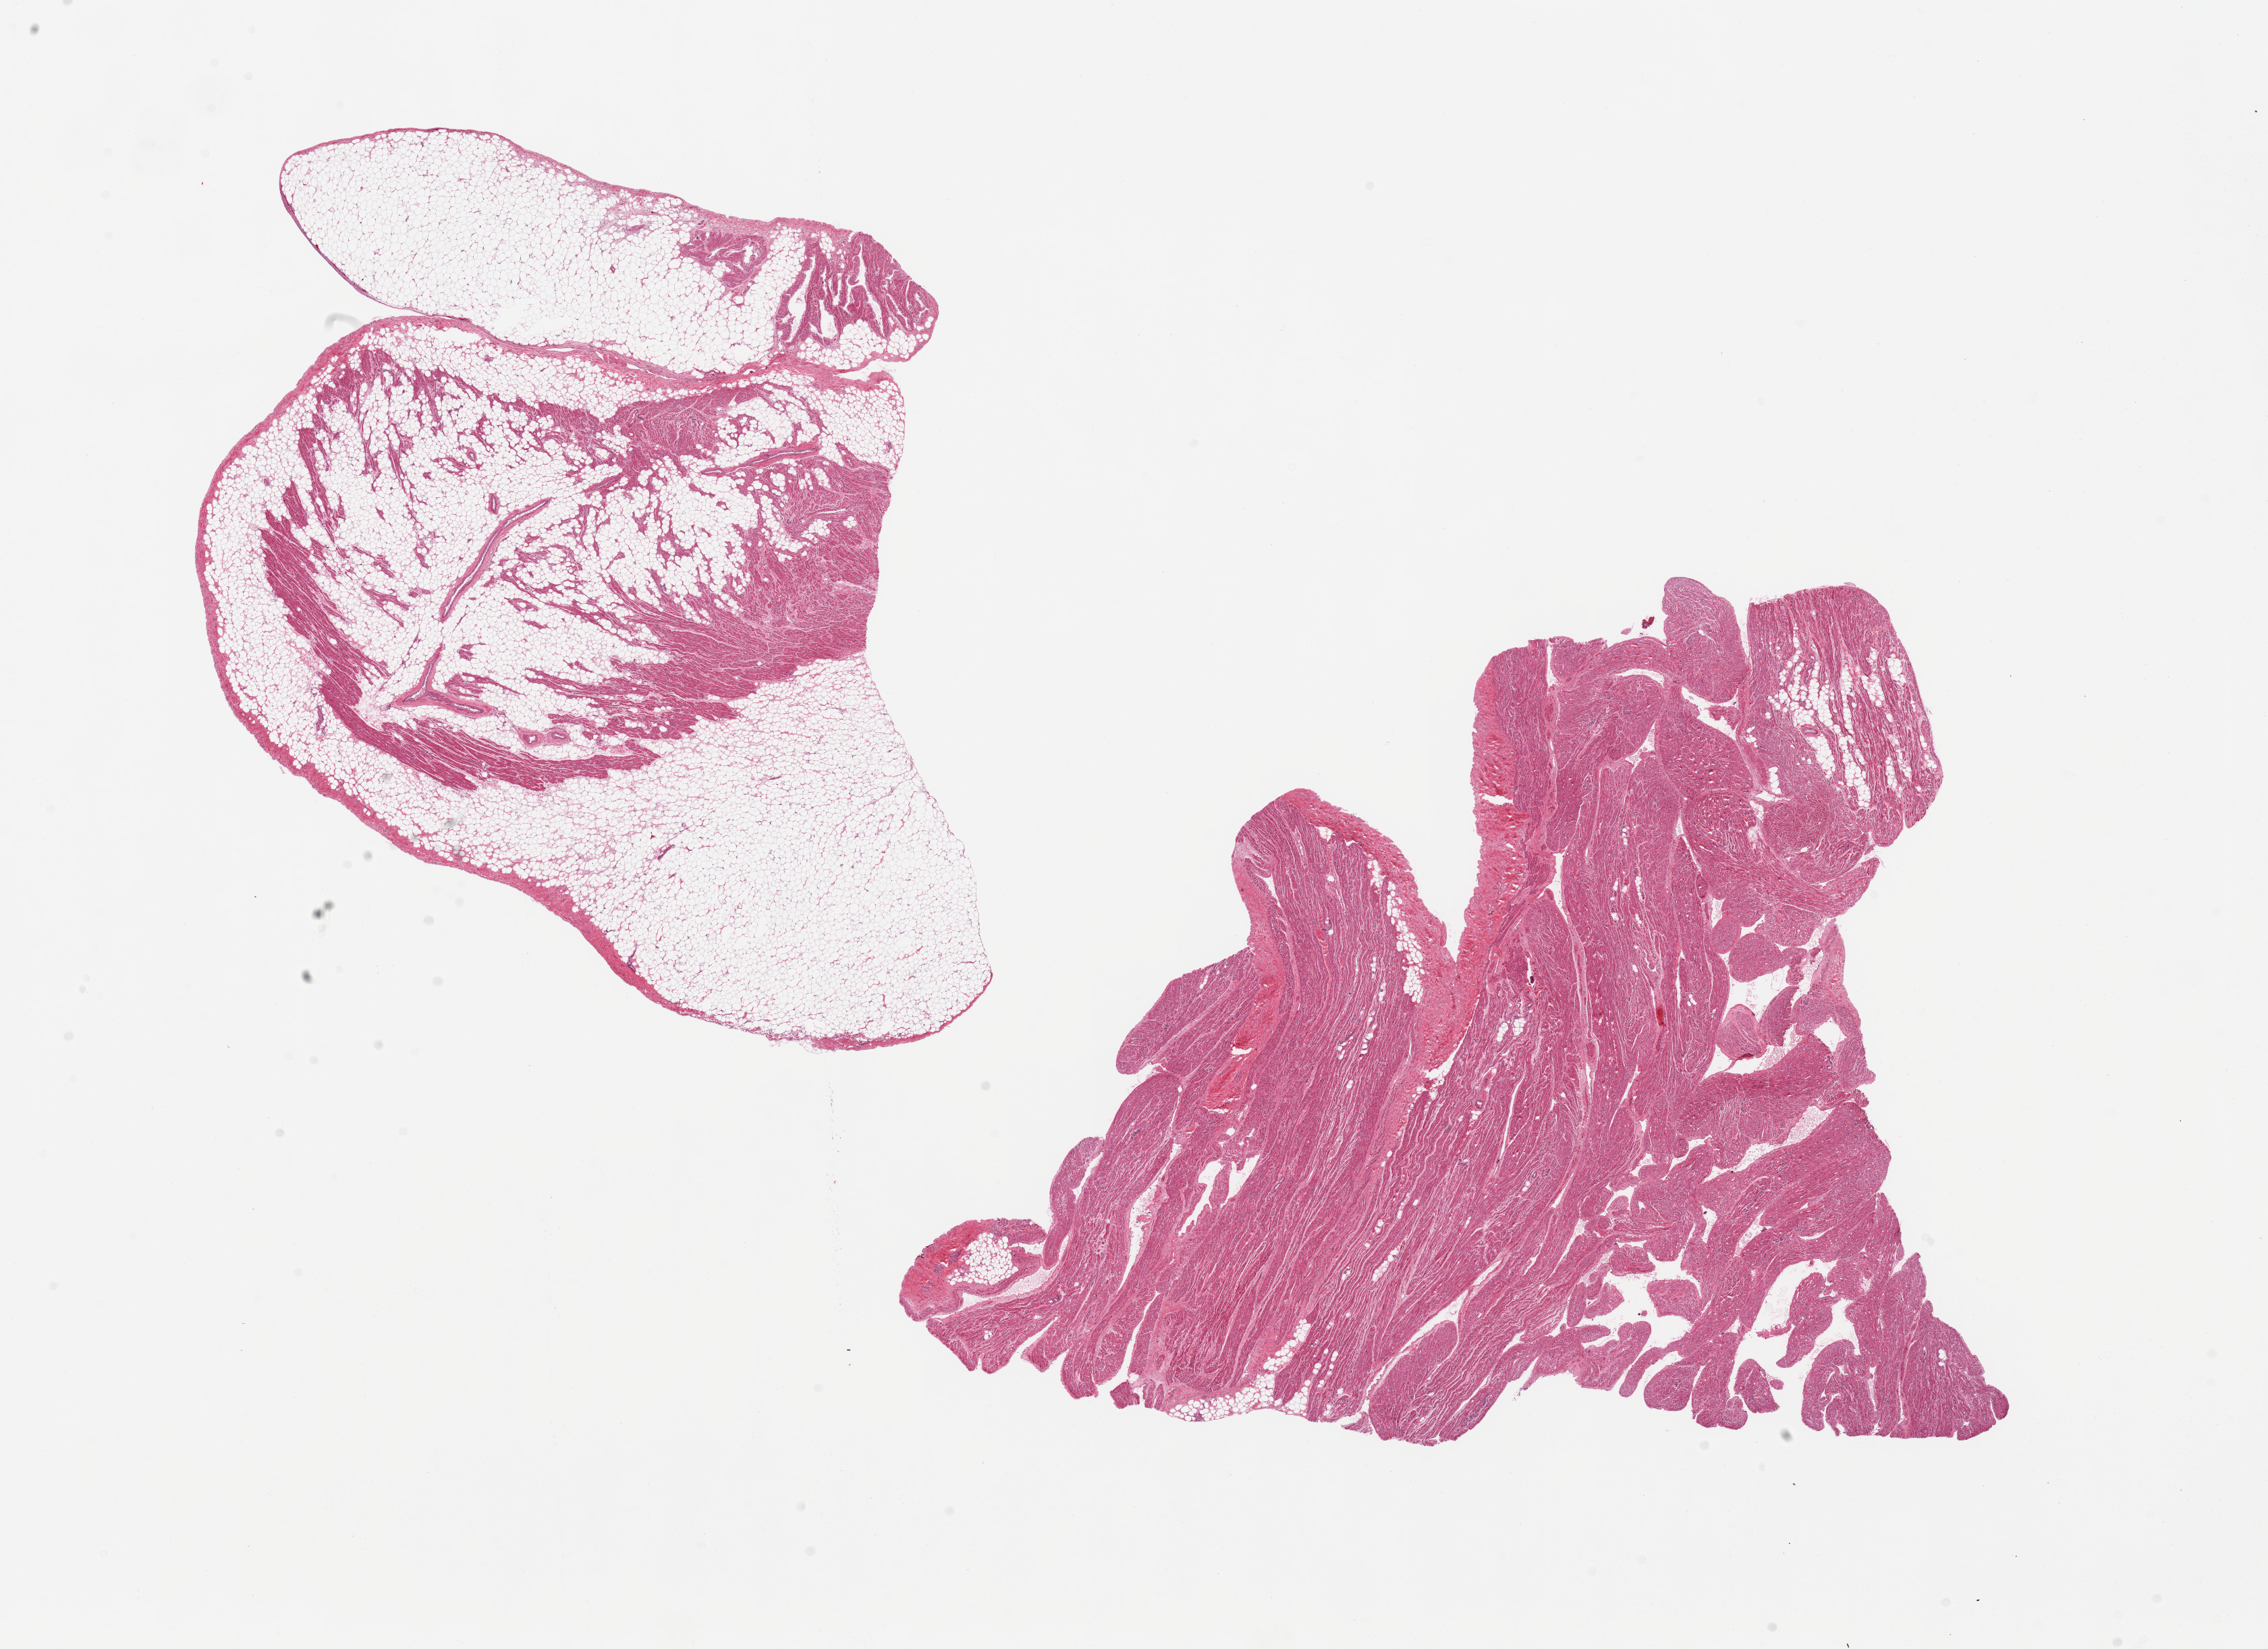
Digitized H&E-stained section, a low-resolution overview of the entire scanned area, about 26.6 x 19.3 mm (acquisition: 20x scan), PAXgene-fixed paraffin-embedded (PFPE) section, sampled site (target tissue): auricular appendage, tissue donor sample. Donor: male.
* pathologist's review note for this sample: 2 pieces, one section is ~50% adherent/ interstitial fat